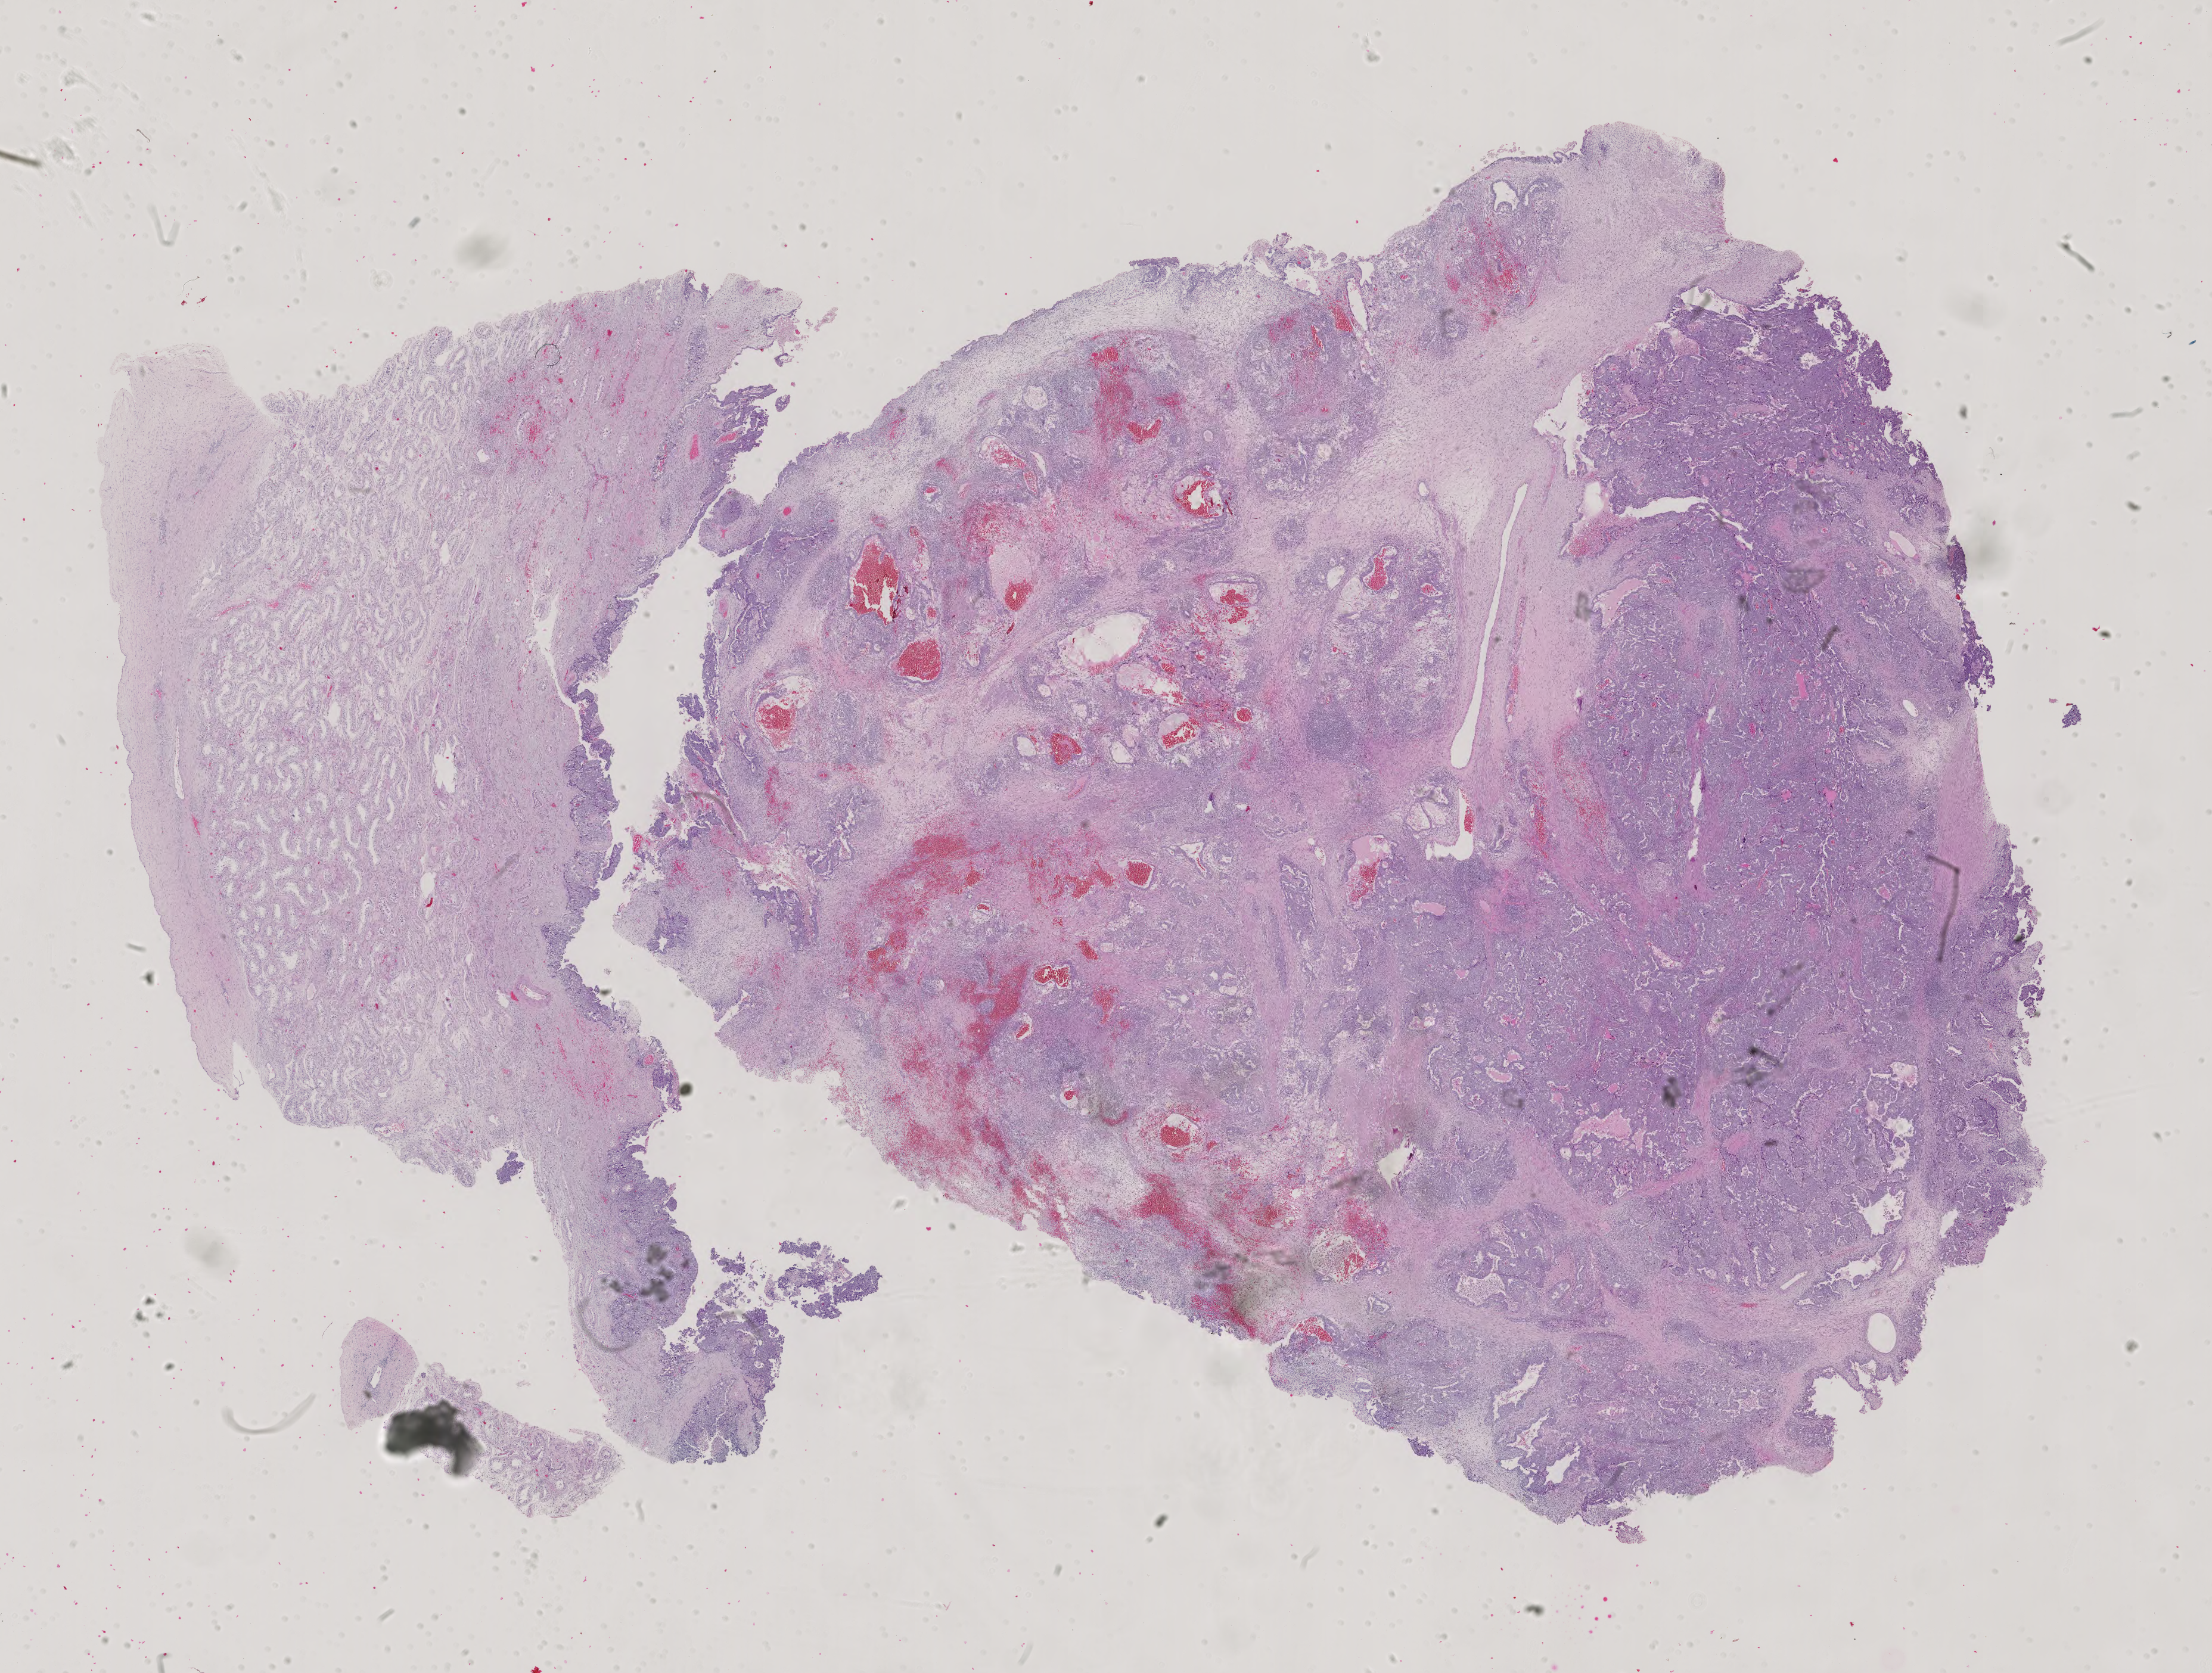
Whole-slide histology image, H&E-stained, a low-resolution overview of the entire scanned area, about 27.0 x 20.5 mm; formalin-fixed paraffin-embedded (FFPE) diagnostic section; sample: primary tumour, testis. Male patient; age at initial diagnosis 28 years.
Histologic diagnosis: Mixed germ cell tumor. AJCC pathologic stage: IS.